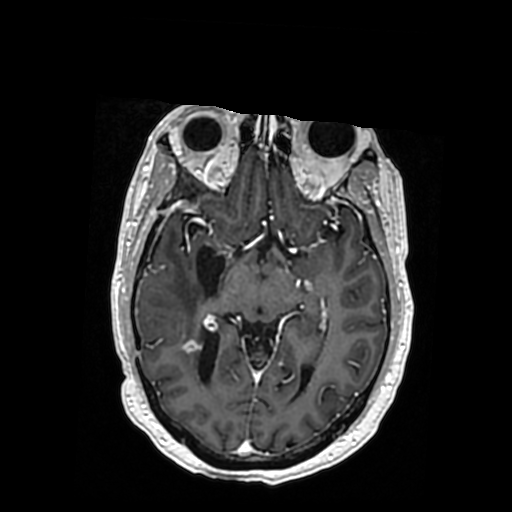
Brain MRI from a brain-tumour surgery series, one axial slice. Position 202 of 364 along the scan axis. T1-weighted post-contrast. 512 × 512 image matrix, field of view 260 × 260 mm. From the clinical record (not read from this slice): histopathology: Oligodendroglioma; WHO grade: 3; IDH mutation: yes.
Annotated regions visible in this slice (outlined manually by an expert reader):
- previous resection cavity: bounding box <196,245,225,297> (left, top, right, bottom; pixels)
- tumour: <146,336,217,348>